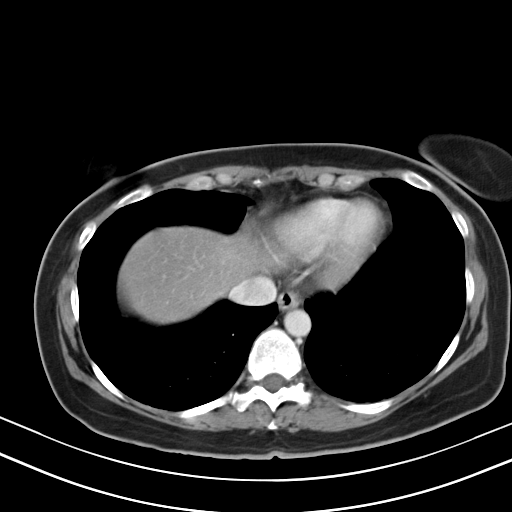
Contrast-enhanced abdominal CT, one axial slice. Position 43 of 47 along the scan axis. Intravenous contrast given. Soft-tissue window (W 400 / L 40 HU). 5 mm slice thickness. 512 × 512 image matrix. Female patient. From the clinical record (not read from this slice): diagnosis: colorectal cancer liver metastases, imaged before liver resection; multiple liver metastases: no; largest metastasis: 3.5 cm; disease in both lobes: no.
Structures marked on this image (outlined manually by an expert reader):
- hepatic veins: bounding box (x1, y1, x2, y2) in pixels: (231, 279, 268, 303)
- liver: (122, 229, 260, 322)
- planned liver remnant (the part of the liver to remain after resection): (122, 229, 261, 321)